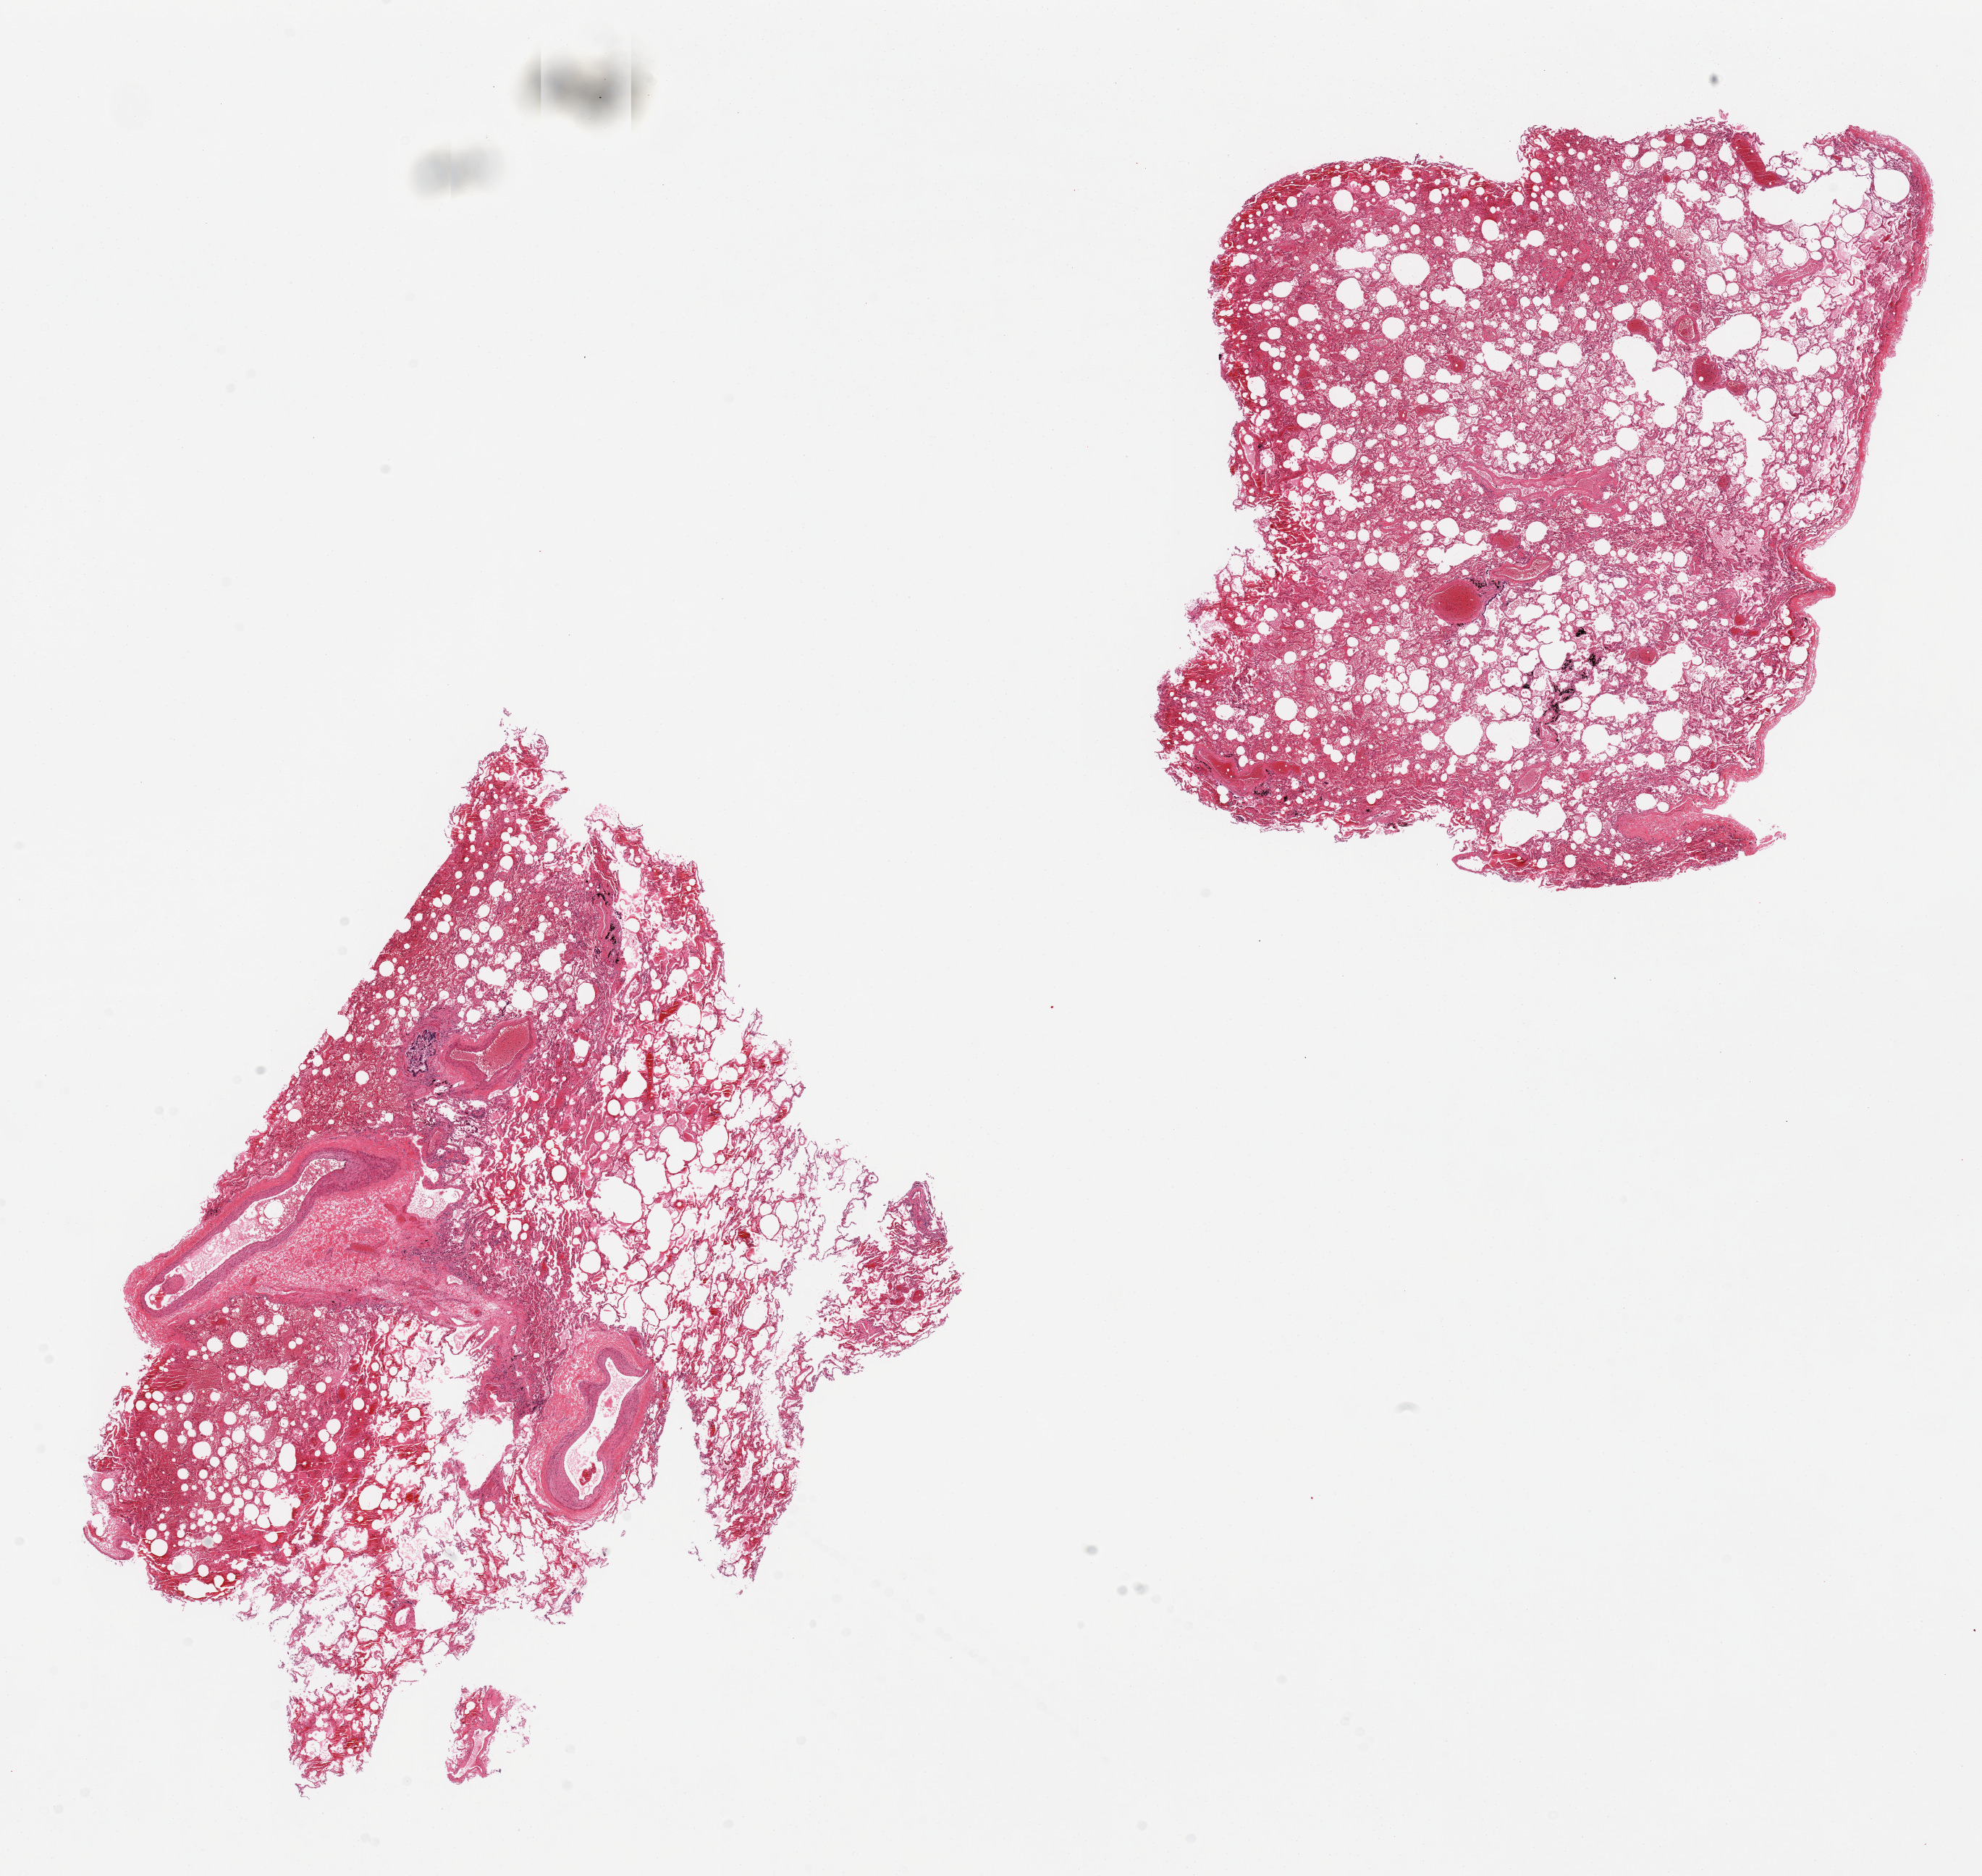
Hematoxylin and eosin (H&E) whole-slide image, brightfield, shown as a low-resolution overview of the whole scanned area (about 21.7 x 20.5 mm, slide scanned at 20x). PAXgene-fixed, paraffin-embedded tissue. Sampled site (target tissue): lung. Tissue donor sample. Male donor.
Review note (as recorded): 2 pieces; patchy alveolar hemorrhage, 20%.